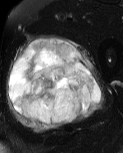
MRI of an extremity soft-tissue mass, one axial slice. Slice 30 of 60 in the series (ordered by position). T2-weighted fat-saturated. MR volume resampled by the dataset authors to the PET/CT grid (not the native acquisition matrix). 3.27 mm slice thickness. 123 × 153 image matrix, field of view 120 × 149 mm. Male patient. From the clinical record (not read from this slice): histological type: pleiomorphic liposarcoma; grade: high; site of the primary tumour: left thigh.
Outlined on this slice (expert contour drawn on MRI and transferred to this co-registered scan by the dataset authors):
- gross tumour volume including surrounding oedema: bounding box <6,34,105,133> (left, top, right, bottom; pixels)
- gross tumour volume (mass): <8,38,101,126>